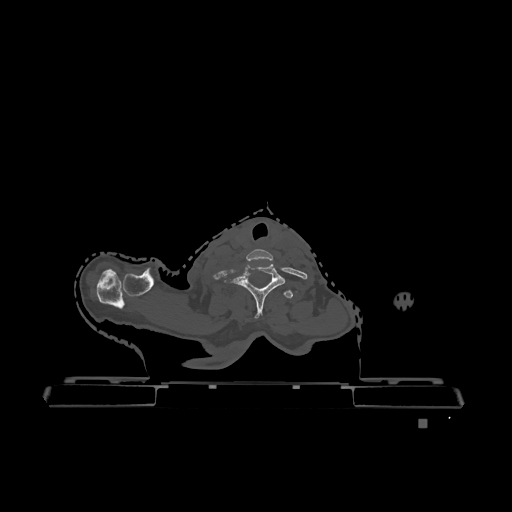
CT including the spine, one axial slice; slice 1027 of 1317 in the series (ordered by position); bone window (W 1800 / L 400 HU); 0.5 mm slice thickness; 512 × 512 image matrix, field of view 500 × 500 mm. Female patient, age 74 years. From the clinical record (not read from this slice): primary cancer: lung.
Outlined on this slice (semi-automatic segmentation, software-assisted and operator-edited):
- T1 vertebra: bounding box [x1, y1, x2, y2] px = [284, 290, 293, 299]